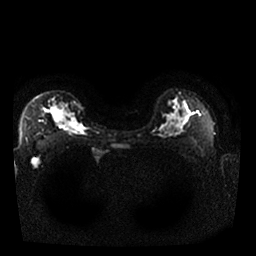
Breast MRI, one axial slice. Slice 19 of 25 in the series (ordered by position). Diffusion-weighted series; image 2 of 4 stored at this slice position (different b-values; order by instance number). 1.5 T. 256 × 256 image matrix, field of view 340 × 340 mm. Female patient.
Outlined on this slice (expert manual segmentation):
- tumour on diffusion-weighted imaging: bounding box (x1, y1, x2, y2) in pixels: (52, 107, 71, 126)